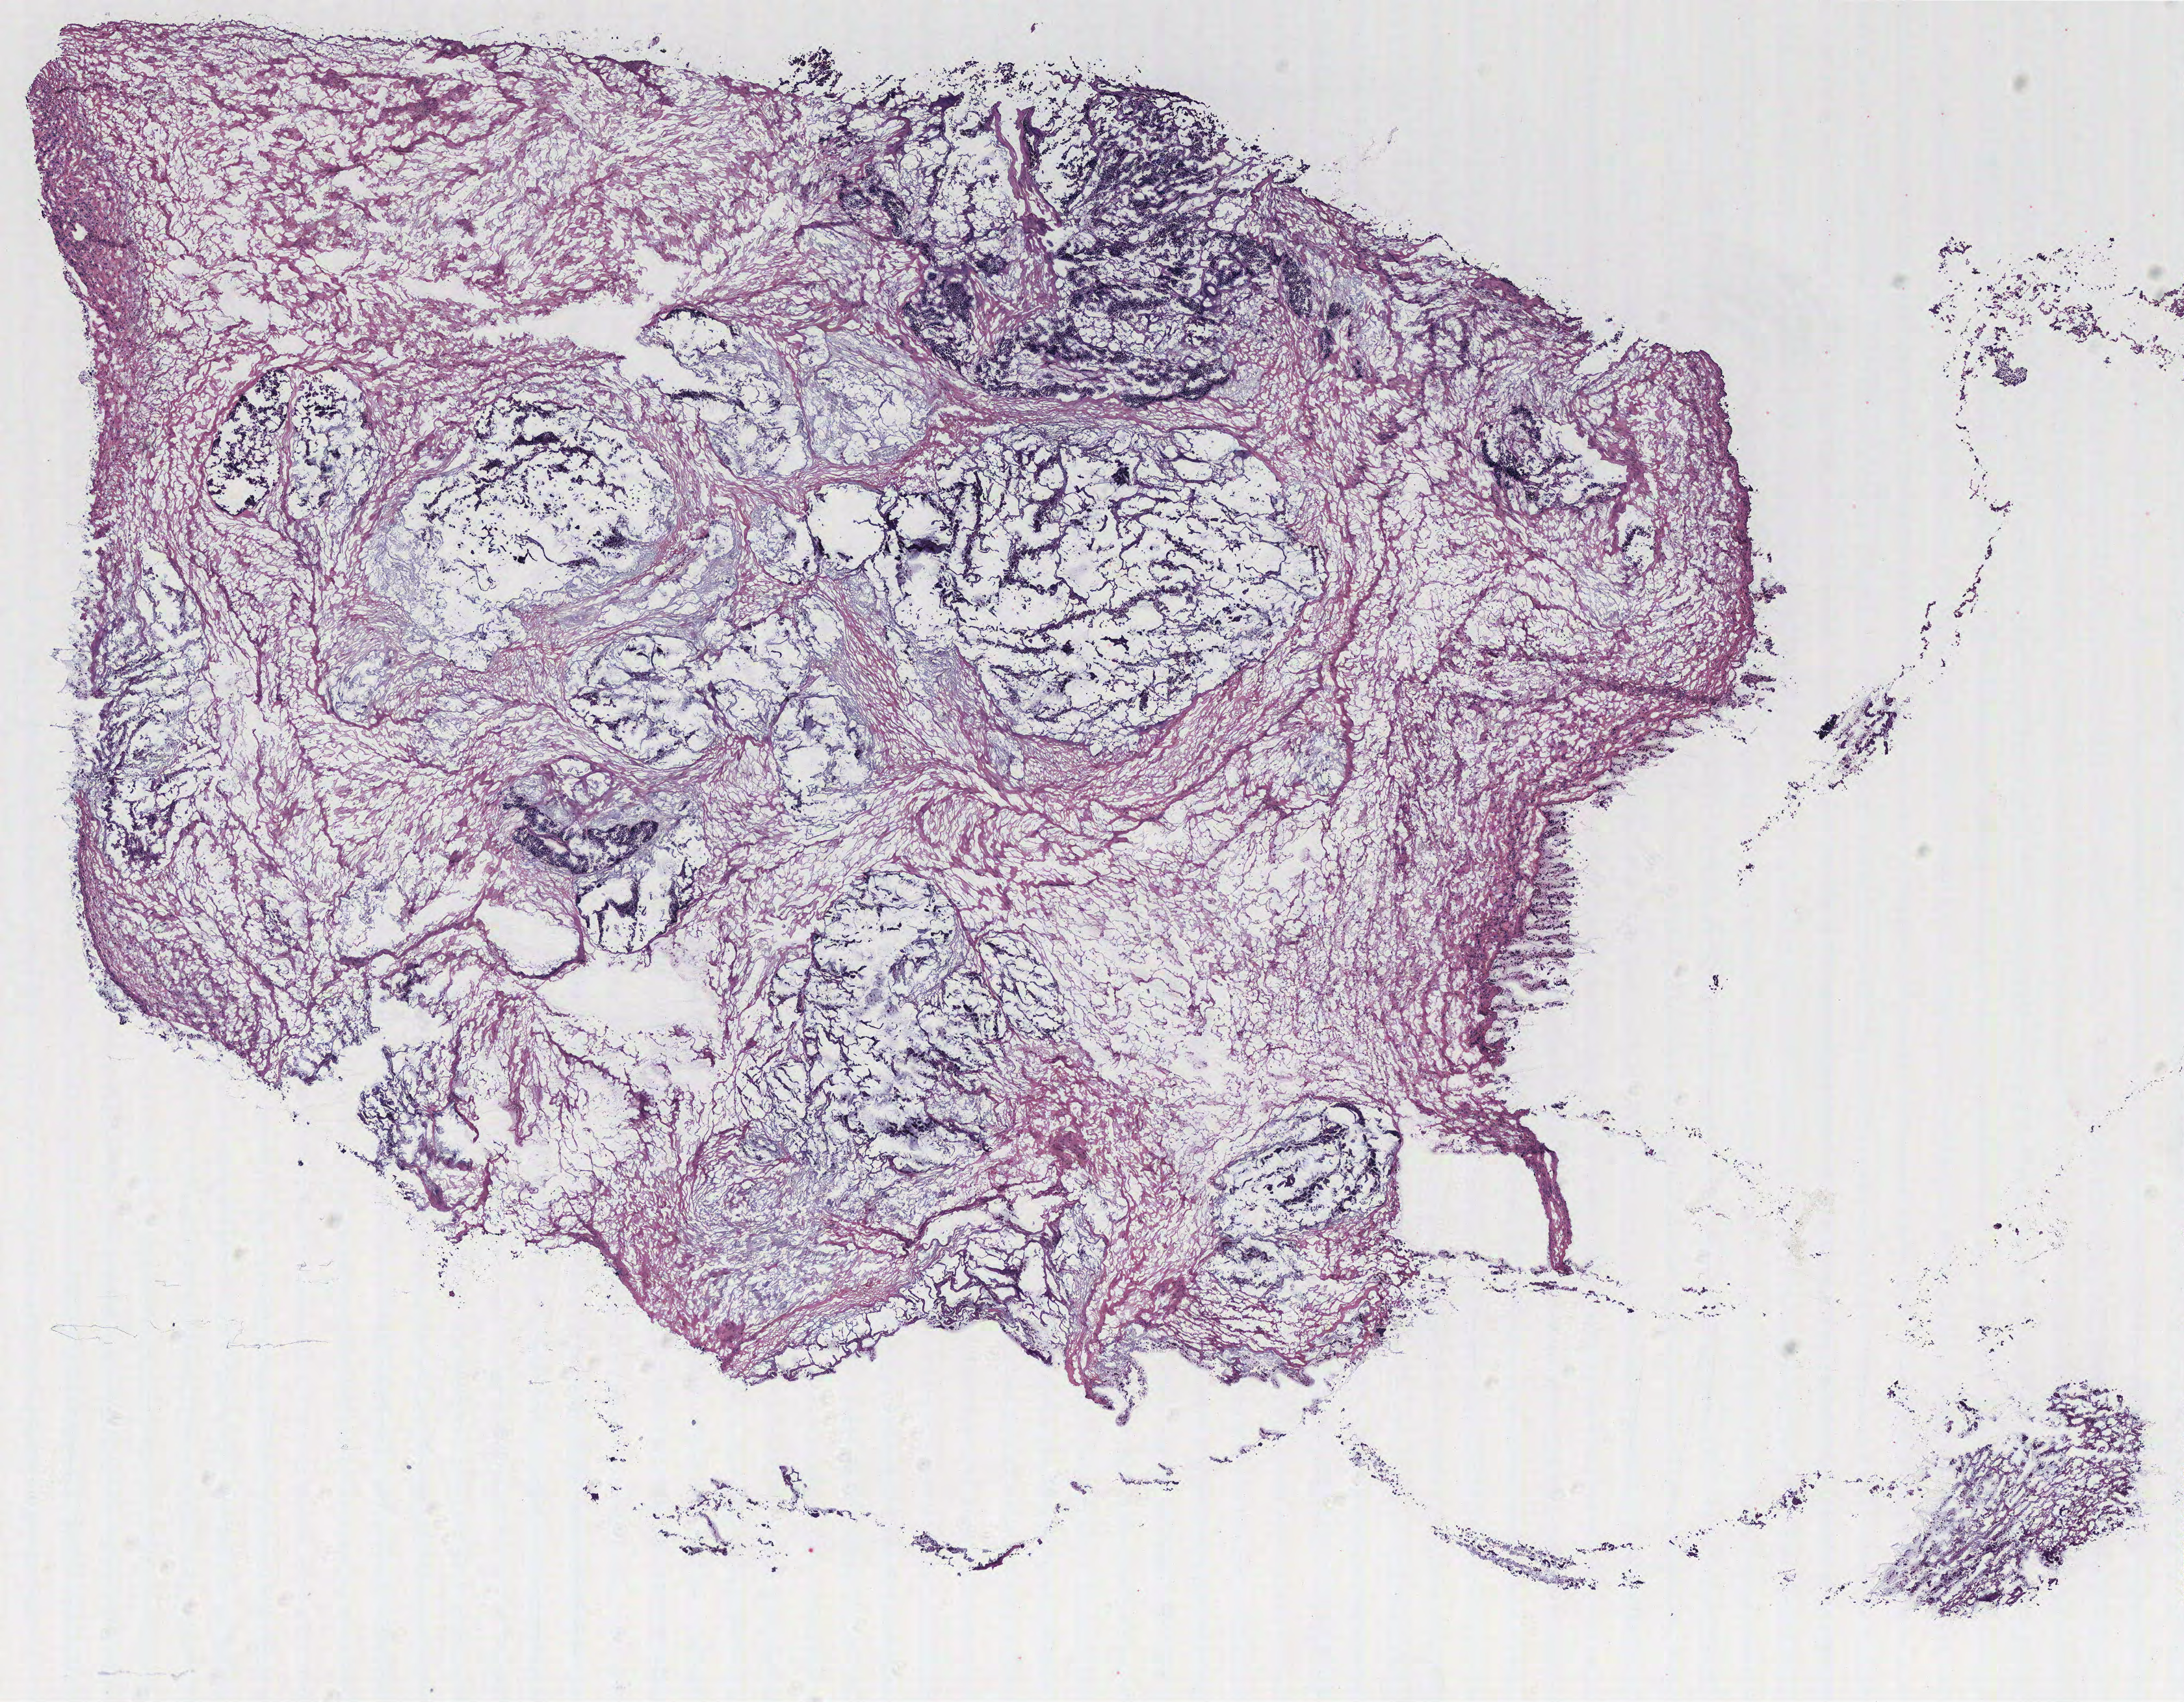
Digitized Hematoxylin and eosin (H&E) stained tissue section (whole slide), shown as a low-resolution overview of the whole scanned area (about 13.4 x 10.5 mm). Tumour tissue sample, ovary. Patient: female, age 57 years.
Primary tumour site (as recorded): ovary. Histologic diagnosis: Serous adenocarcinoma, NOS.